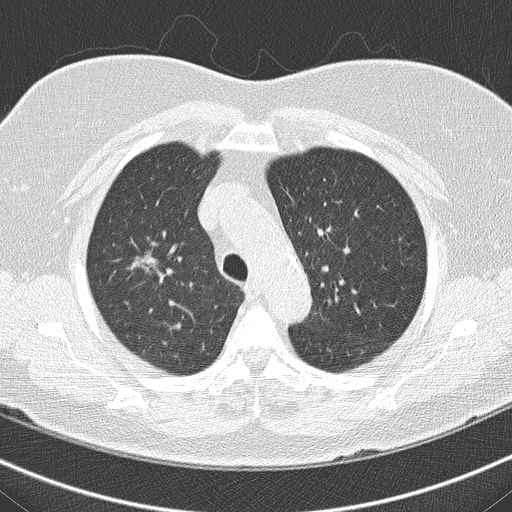
Axial slice from a low-dose chest CT screening exam. Third screening round (two years after baseline). Lung window (W 1500 / L -600 HU). Lung (sharp) reconstruction kernel (B50f). 120 kVp. Slice 133 of 161 in the series. Female, age 74 years at enrolment. Former smoker at enrolment.
Lesion marked by an expert reader, bounding box [x1, y1, x2, y2] px = [112, 237, 181, 298]. The screening reader recorded 5 non-calcified nodules or masses ≥4 mm on this exam (right upper lobe, right middle lobe, right middle lobe, left lower lobe, right lower lobe); which of them this box marks is not recorded. Later outcome: lung cancer diagnosed 117 days after this screen — bronchiolo-alveolar carcinoma, non-mucinous, right upper lobe, well differentiated (G1), stage IA (AJCC 6th edition), 14 mm at pathology.